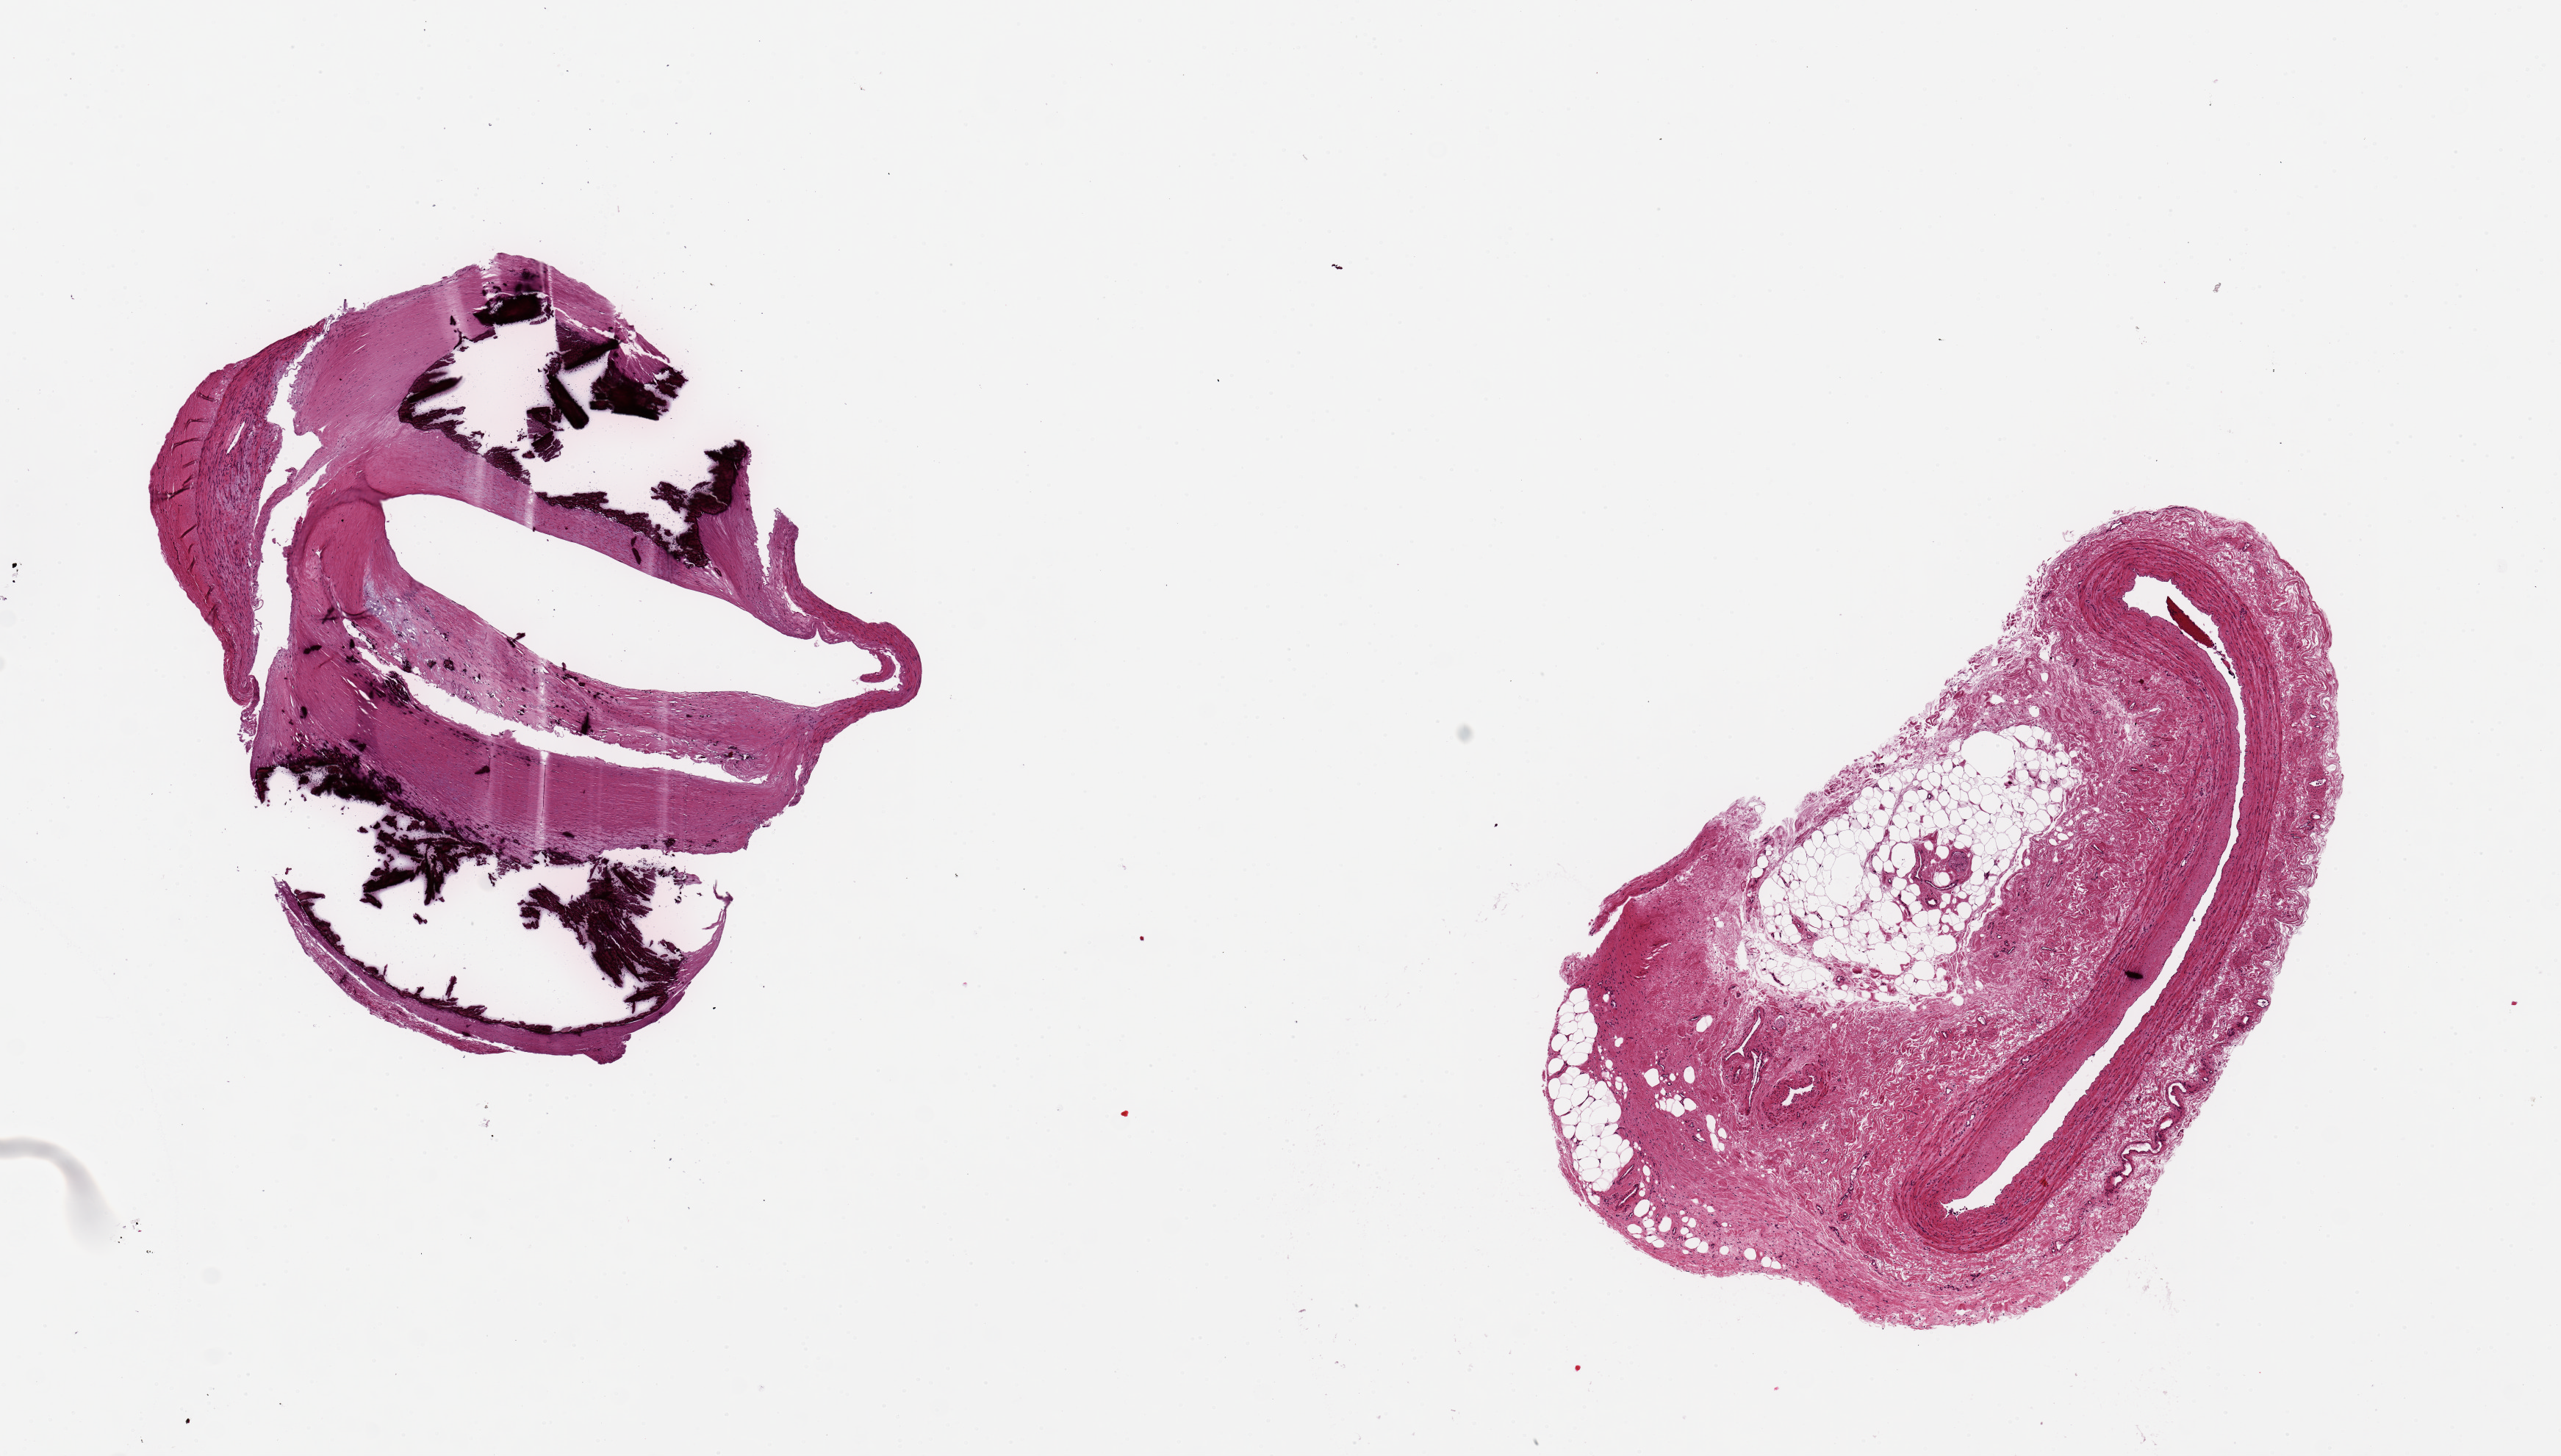
Whole-slide image, hematoxylin and eosin (H&E) stain, shown as a low-resolution overview of the whole scanned area (about 13.8 x 7.8 mm), PAXgene-fixed paraffin-embedded (PFPE) section, section of tibial artery (target tissue), tissue donor sample. Male donor.
Reviewer comment on this tissue sample: 2 pieces, 4x4 & 5x3mm; 1 severely calcified, 1 without lesions but with 60% peripheral fibroadipose.